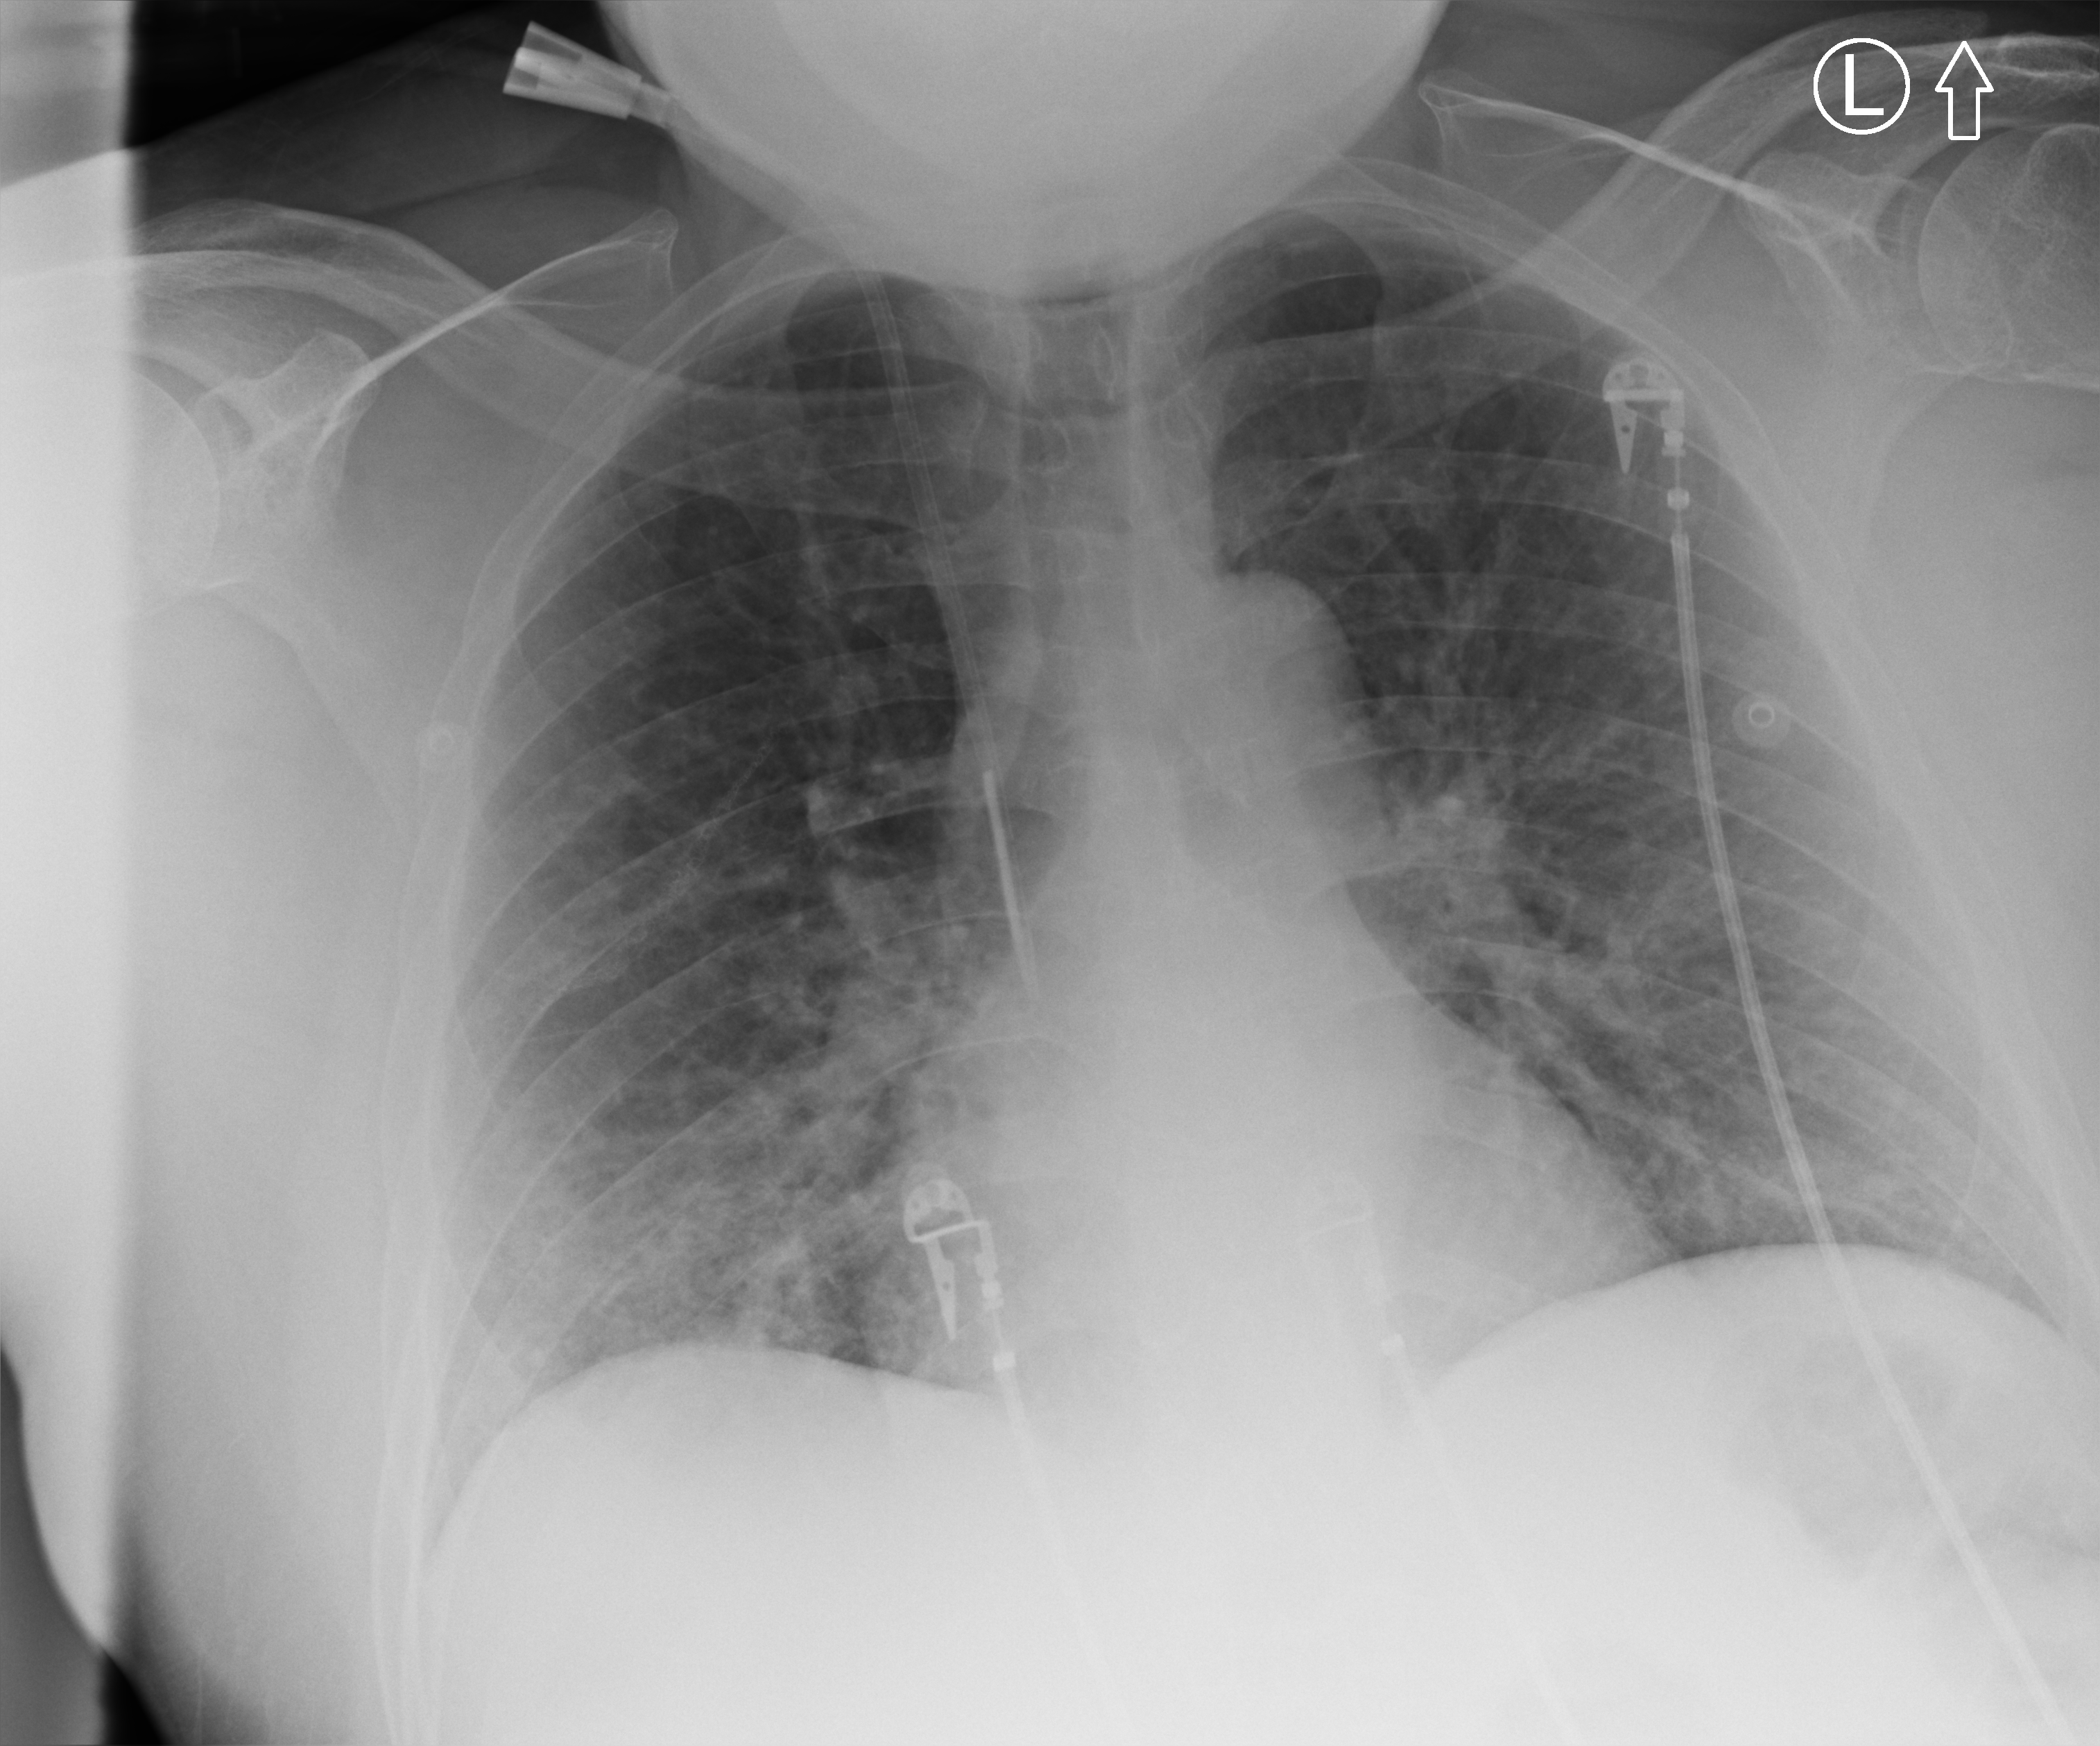
Portable chest radiograph, anteroposterior (AP) projection. Male patient hospitalised with COVID-19, age 18–59 years.
Hospital-stay facts (about this admission, not read from this image; timing relative to this image not recorded): chronic kidney disease (admission record): no.